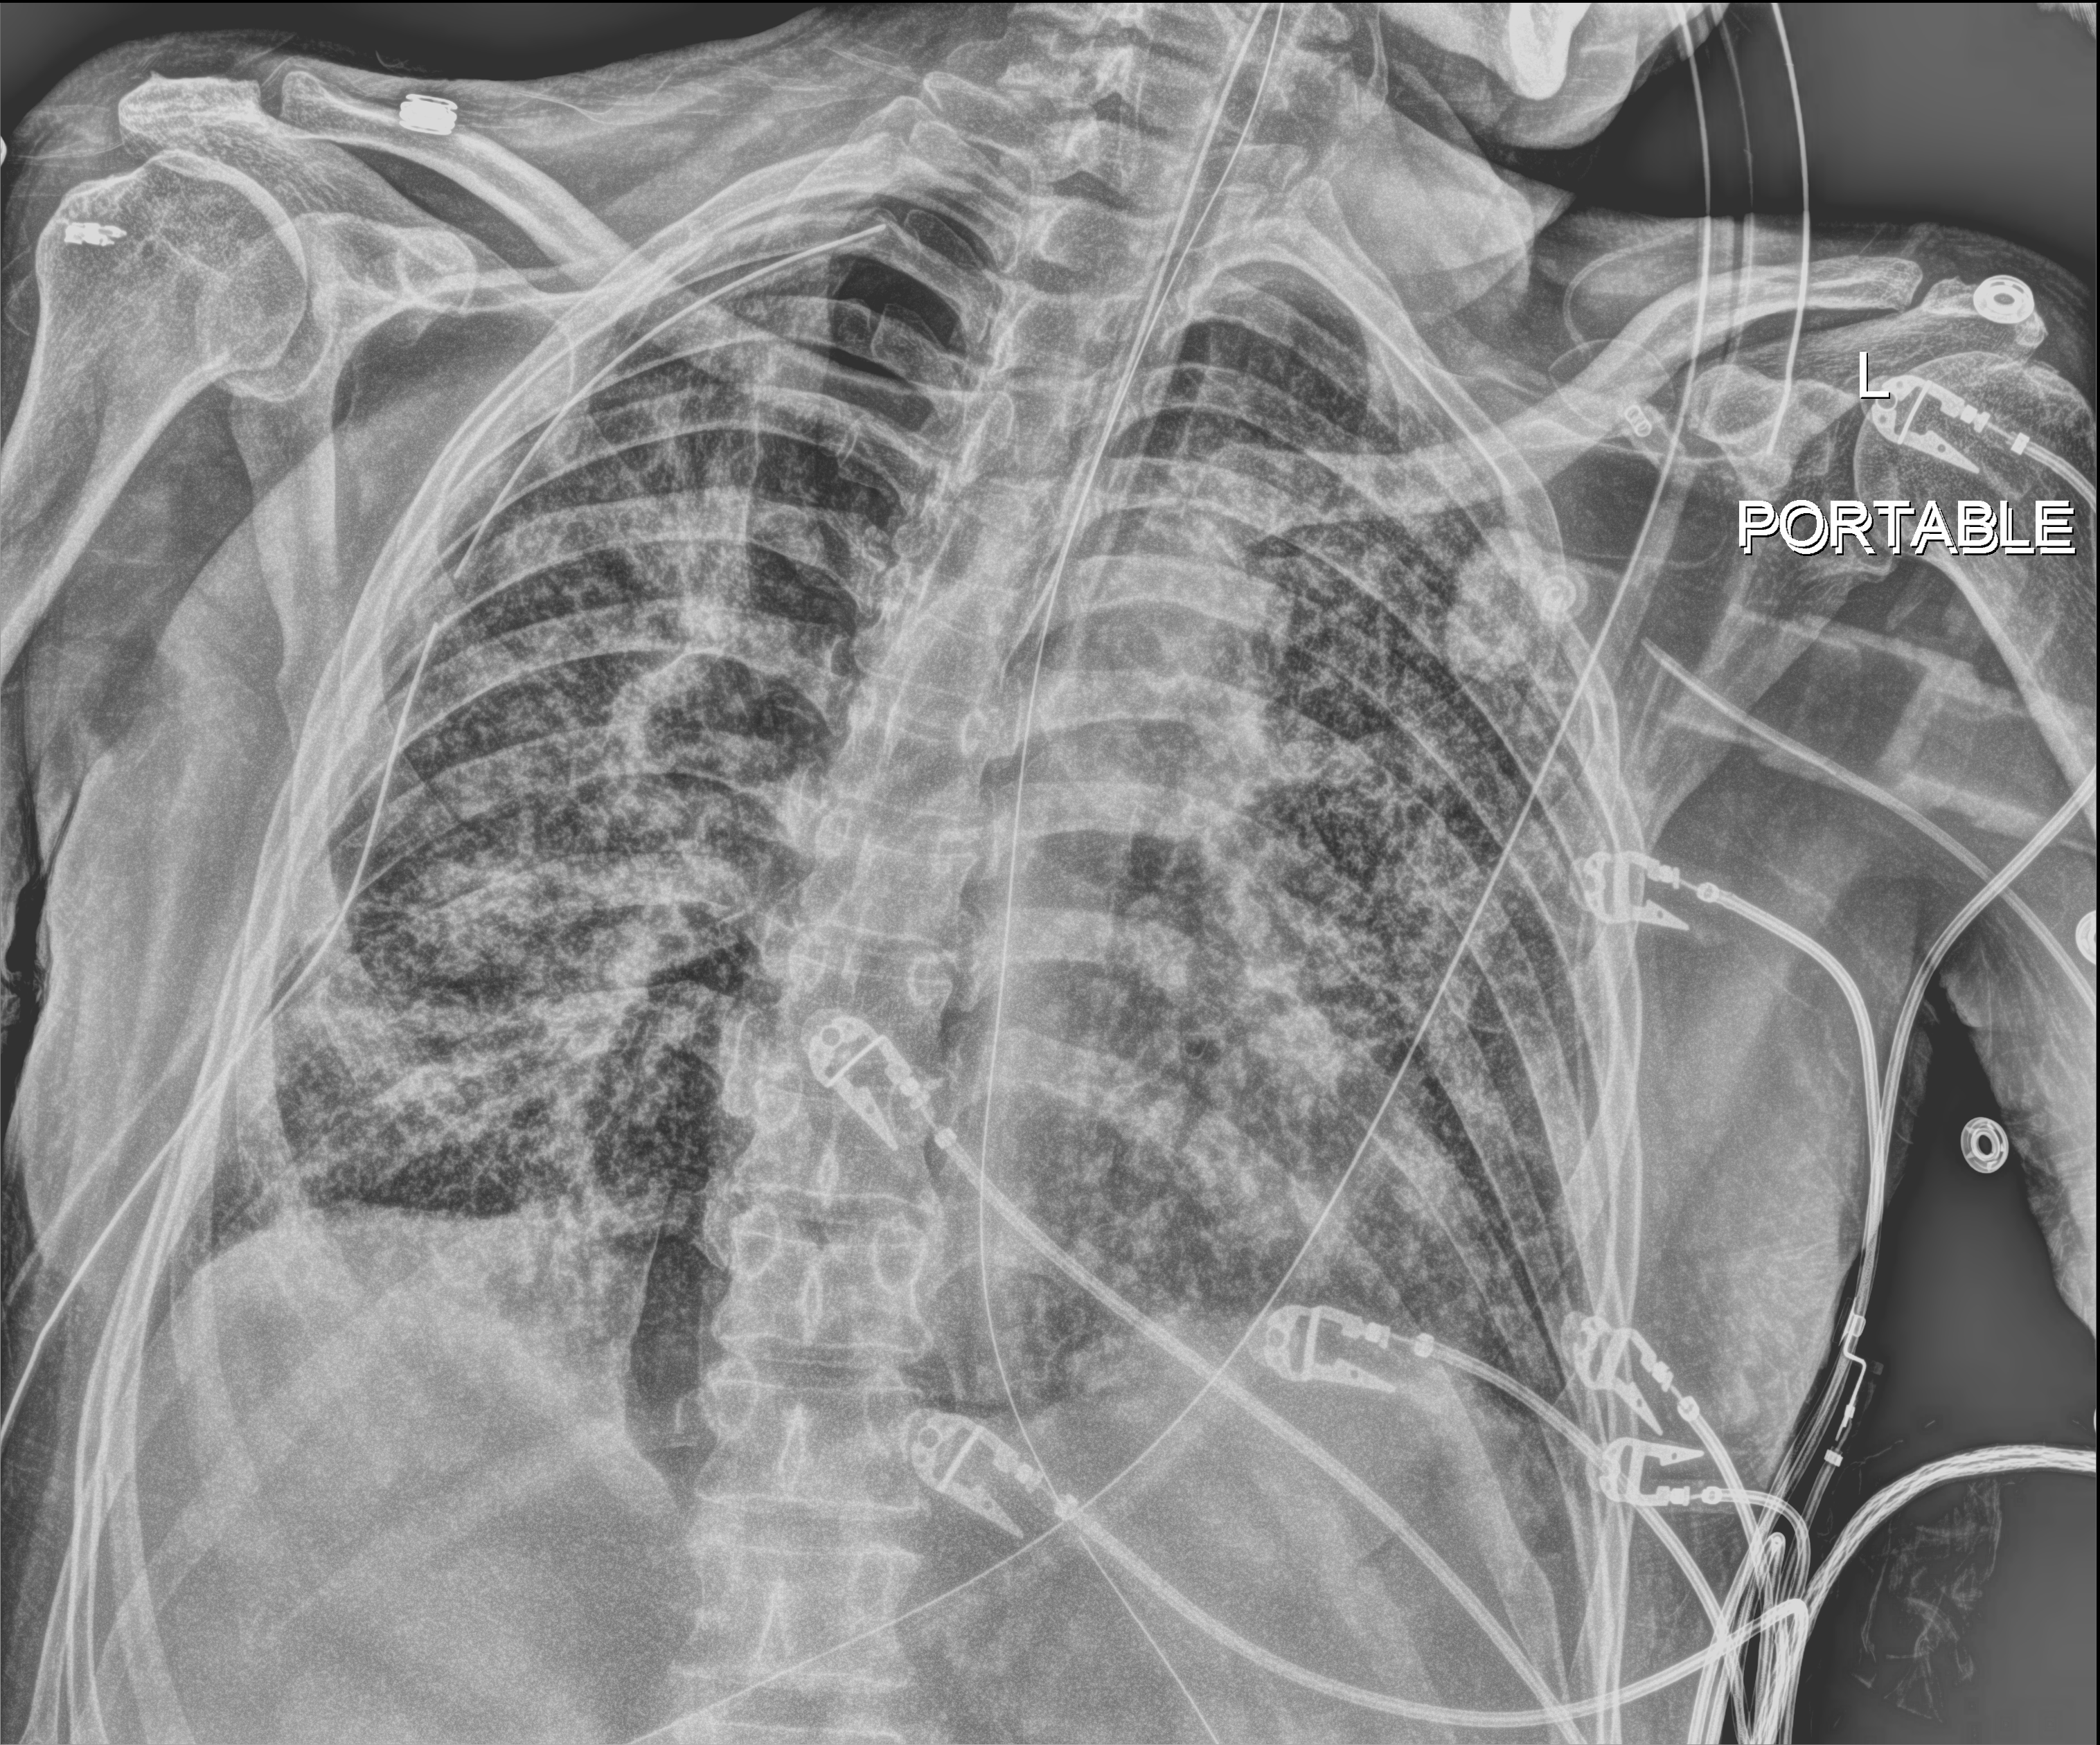
Bedside chest radiograph (digital radiography). Male patient hospitalised with COVID-19, age 60–74 years.
Hospital-stay facts (about this admission, not read from this image; timing relative to this image not recorded): mechanically ventilated during this hospital stay: yes.